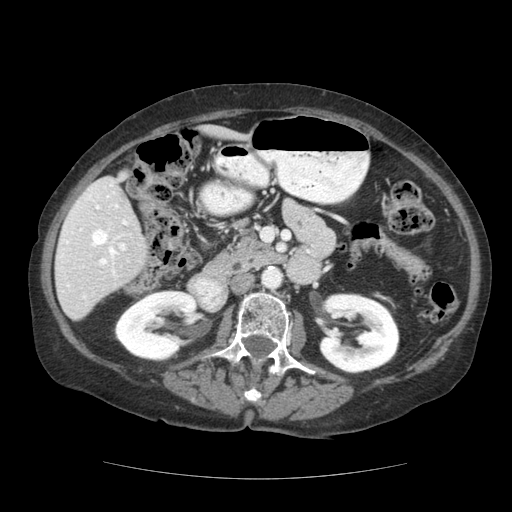
Contrast-enhanced abdominal CT (liver protocol), one axial slice. Position 56 of 111 along the scan axis. 140 kVp. Soft-tissue window (W 400 / L 40 HU). 2.5 mm slice thickness. 512 × 512 image matrix, field of view 360 × 360 mm. From the clinical record (not read from this slice): diagnosis: hepatocellular carcinoma (patient treated with transarterial chemoembolisation; whether this scan precedes or follows treatment is not stated here); TNM stage (as recorded): Stage-I; Child-Pugh class: A; tumour differentiation: moderately-poorly differentiated.
Annotated regions visible in this slice (semi-automatic segmentation, software-assisted and operator-edited):
- liver parenchyma outside the tumour (the mass and vessels are separate outlines, so this box may not span the whole liver): bounding box [x1, y1, x2, y2] px = [54, 126, 244, 320]
- liver vessels: [59, 181, 128, 299]